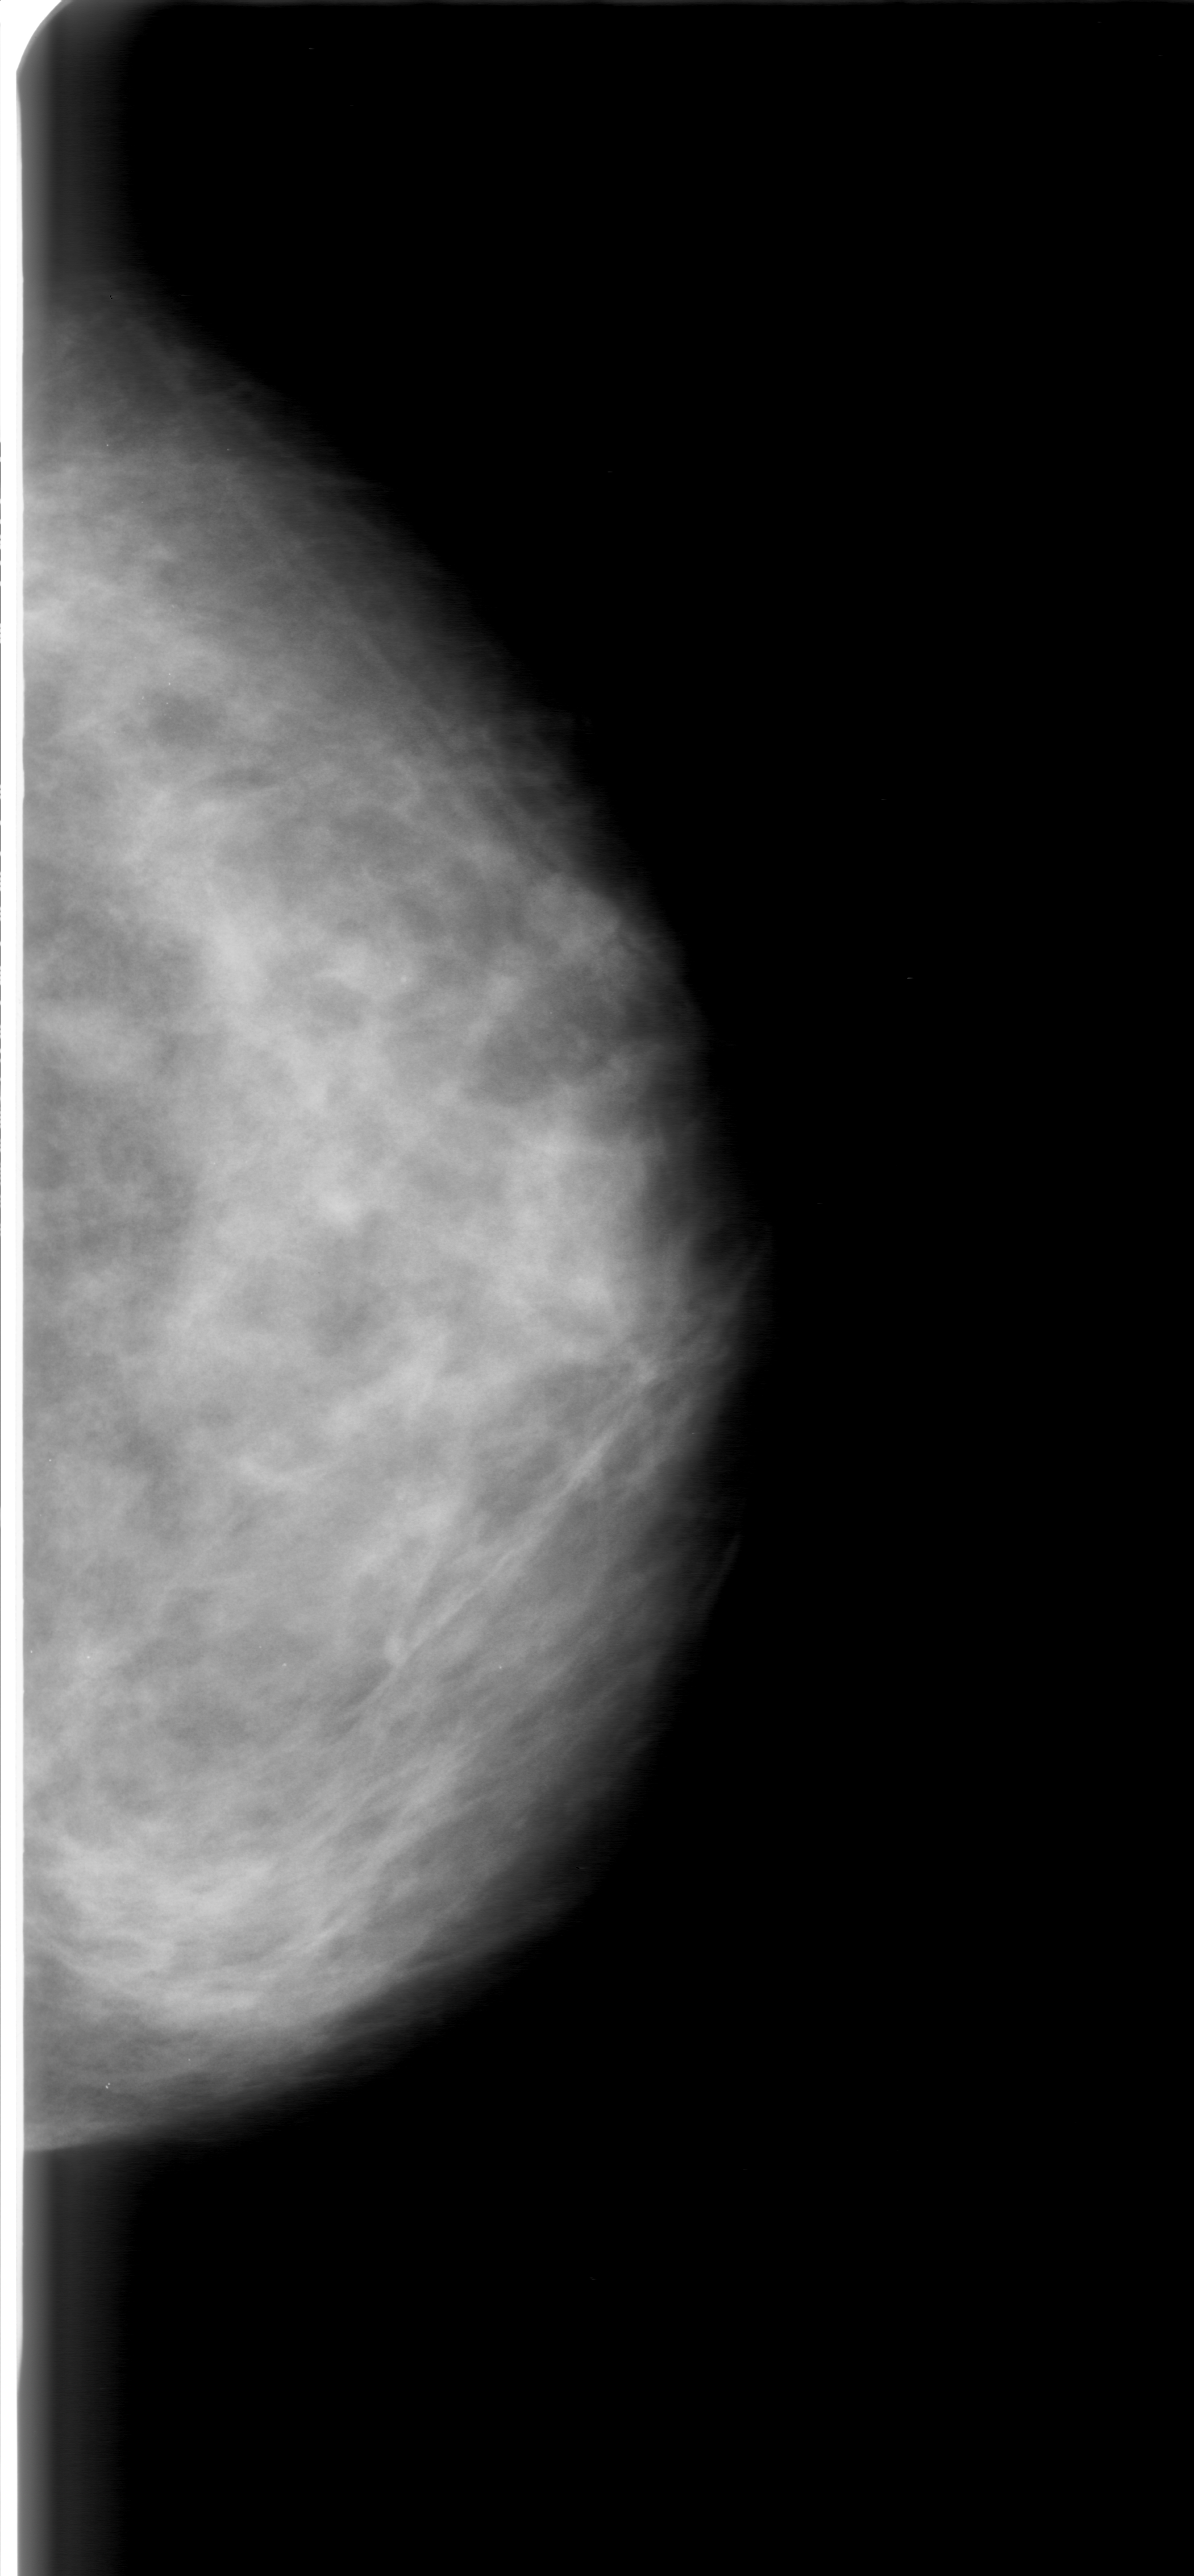
Scanned film-screen mammogram; left breast; CC view; BI-RADS breast density category 3 (scale 1–4); 1194 × 2576 image matrix.
Expert-marked regions of interest on this film, with their recorded descriptors:
- mass, shape lobulated, margins microlobulated; BI-RADS assessment category 0; pathology (as recorded): benign: bounding box [x1, y1, x2, y2] px = [451, 843, 671, 1046]